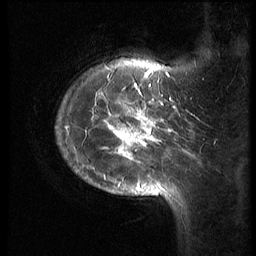
Breast MRI (dynamic contrast-enhanced), one sagittal slice; slice 14 of 70 in the series (ordered by position); 3 images stored at this slice position (order not interpretable as contrast timing); 1.5 T; TE 4.2 ms, TR 9 ms; 256 × 256 image matrix, field of view 180 × 180 mm. Patient: female, 28 years. Case-level facts recorded for this patient, not image findings: setting: breast cancer imaged before/during neoadjuvant chemotherapy.
Structures marked on this image (semi-automatically segmented with operator editing):
- analysis volume of interest (the breast-tissue region the enhancement analysis was run in; not a lesion): bounding box [x1, y1, x2, y2] px = [58, 47, 186, 215]
- tumour enhancement mask (voxels above the 140 % enhancement threshold inside the analysis volume of interest): [77, 62, 177, 197]